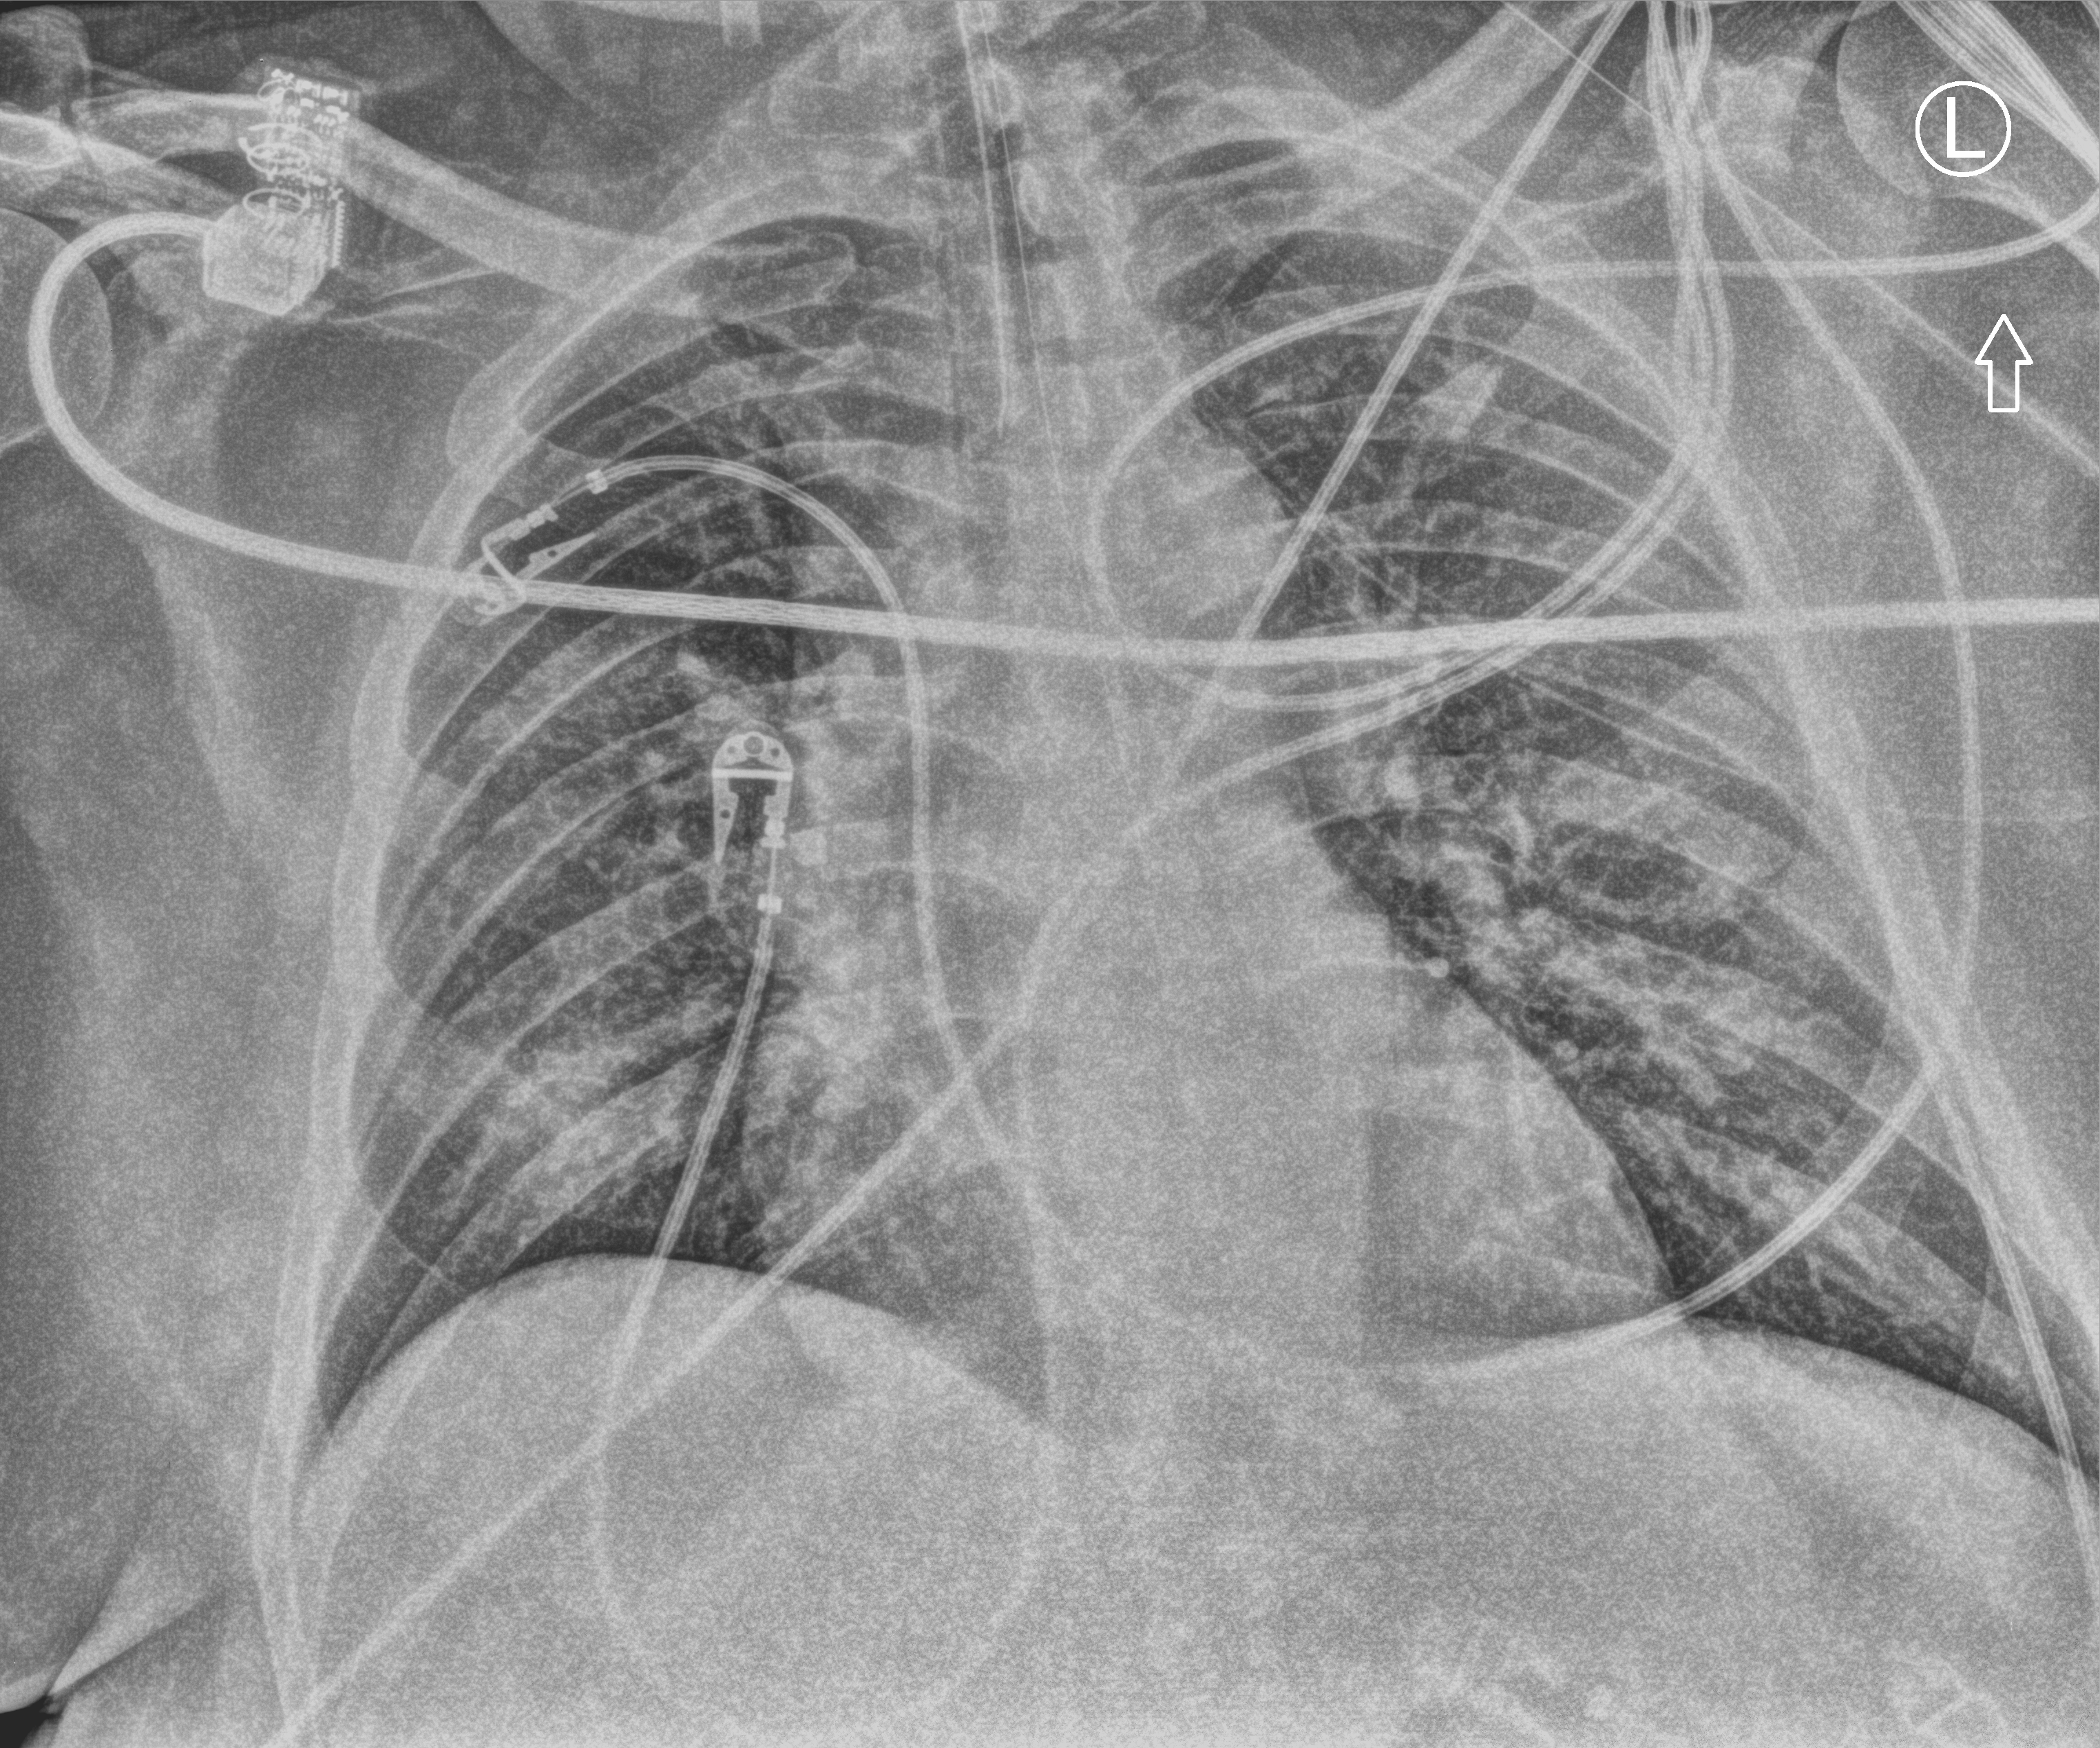
Chest X-ray (portable), anteroposterior (AP) projection. Male patient hospitalised with COVID-19, age 60–74 years.
Admission-level facts for this patient (not findings on this image; timing relative to this image not recorded):
- diabetes (admission record): yes
- smoking status (admission record): former